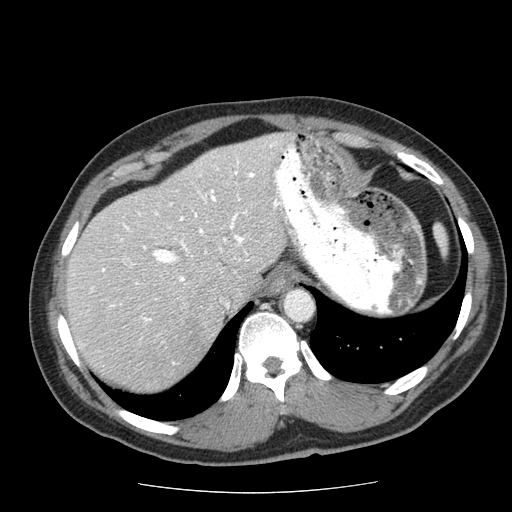
Contrast-enhanced abdominal CT (liver protocol), one axial slice. Position 47 of 85 along the scan axis. 120 kVp. Soft-tissue window (W 400 / L 40 HU). 2.5 mm slice thickness. 512 × 512 image matrix, field of view 360 × 360 mm. Case-level facts recorded for this patient, not image findings: diagnosis: hepatocellular carcinoma (patient treated with transarterial chemoembolisation; whether this scan precedes or follows treatment is not stated here); TNM stage (as recorded): Stage-IIIA; Child-Pugh class: A; tumour differentiation: well differentiated; tumour nodularity: multinodular.
Outlined on this slice (semi-automatically segmented with operator editing):
- liver parenchyma outside the tumour (the mass and vessels are separate outlines, so this box may not span the whole liver): box from (x=66, y=134) to (x=296, y=390) px
- mass: (x=168, y=283)–(x=228, y=371)
- liver vessels: (x=73, y=142)–(x=295, y=364)